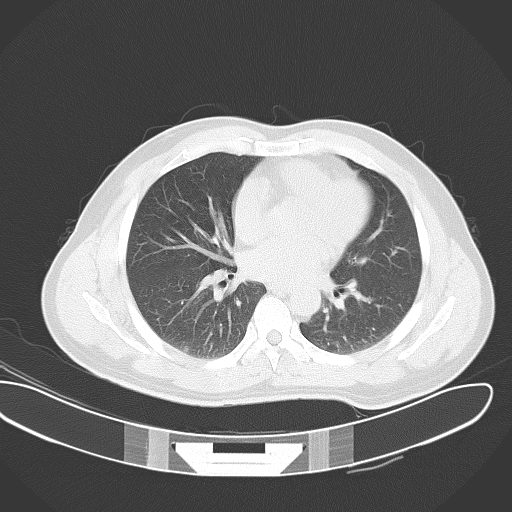
Chest CT, one axial slice; slice 18 of 45 in the series (ordered by position); reconstruction kernel B70f; lung window (W 1500 / L -600 HU); 5 mm slice thickness; 512 × 512 image matrix, field of view 403 × 403 mm. Patient: male, 54 years. Case-level facts recorded for this patient, not image findings: clinical TNM (as recorded): Tis N0 M0.
Structures marked on this image (bounding box drawn by a radiologist):
- lung tumour (recorded histology: adenocarcinoma): bounding box [x1, y1, x2, y2] px = [181, 342, 194, 354]